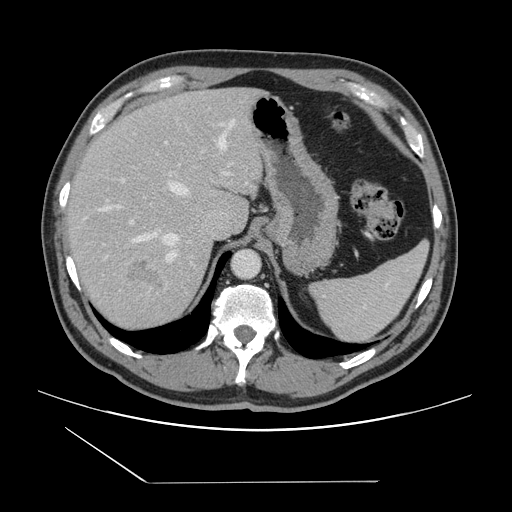
Contrast-enhanced abdominal CT, one axial slice; slice 109 of 157 in the series (ordered by position); 120 kVp; intravenous contrast given; soft-tissue window (W 400 / L 40 HU); 2.5 mm slice thickness; 512 × 512 image matrix, field of view 407 × 407 mm. Male patient, age 61 years. Case-level facts recorded for this patient, not image findings: diagnosis: colorectal cancer liver metastases, imaged before liver resection; multiple liver metastases: yes; largest metastasis: 5.5 cm; disease in both lobes: yes.
Outlined on this slice (manually delineated by an expert):
- hepatic veins: bounding box <103,120,234,264> (left, top, right, bottom; pixels)
- liver: <63,88,262,331>
- planned liver remnant (the part of the liver to remain after resection): <66,88,237,230>
- portal vein (with intrahepatic branches): <122,141,230,224>
- liver metastasis: <124,258,172,298>